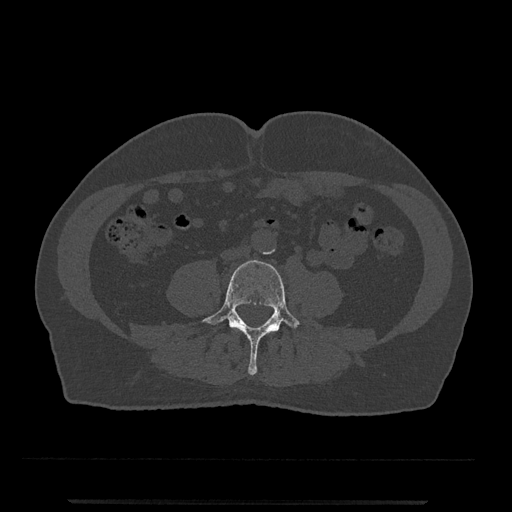
CT including the spine, one axial slice; slice 141 of 797 in the series (ordered by position); bone window (W 1800 / L 400 HU); 0.5 mm slice thickness; 512 × 512 image matrix, field of view 419 × 419 mm. Patient: male, 63 years. From the clinical record (not read from this slice): primary cancer: prostate.
Annotated regions visible in this slice (semi-automatic segmentation, software-assisted and operator-edited):
- L4 vertebra: bounding box [x1, y1, x2, y2] px = [201, 260, 301, 375]